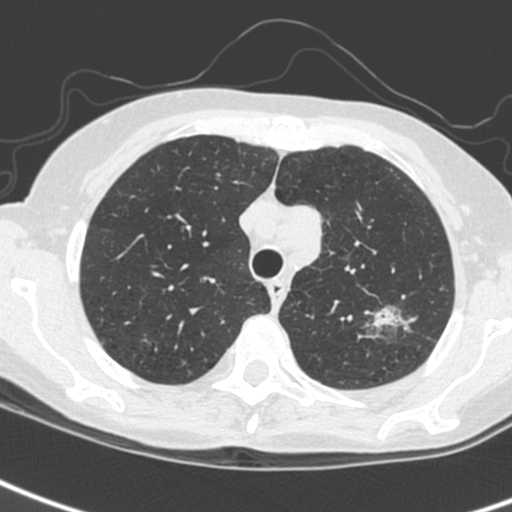
Chest CT (low-dose screening protocol), one axial image, first (baseline) screen, lung window (W 1500 / L -600 HU), slice 43 of 242 in the series, 512 × 512 image matrix. Female participant, aged 61 years at enrolment. Current smoker at enrolment.
Expert-annotated lung lesion, box from (x=349, y=299) to (x=412, y=349) px. The screening reader recorded 2 non-calcified nodules or masses ≥4 mm on this exam (left upper lobe, left upper lobe); which of them this box marks is not recorded. Later outcome: lung cancer diagnosed 29 days after this screen — small cell carcinoma, NOS, left upper lobe, stage IV (AJCC 6th edition).